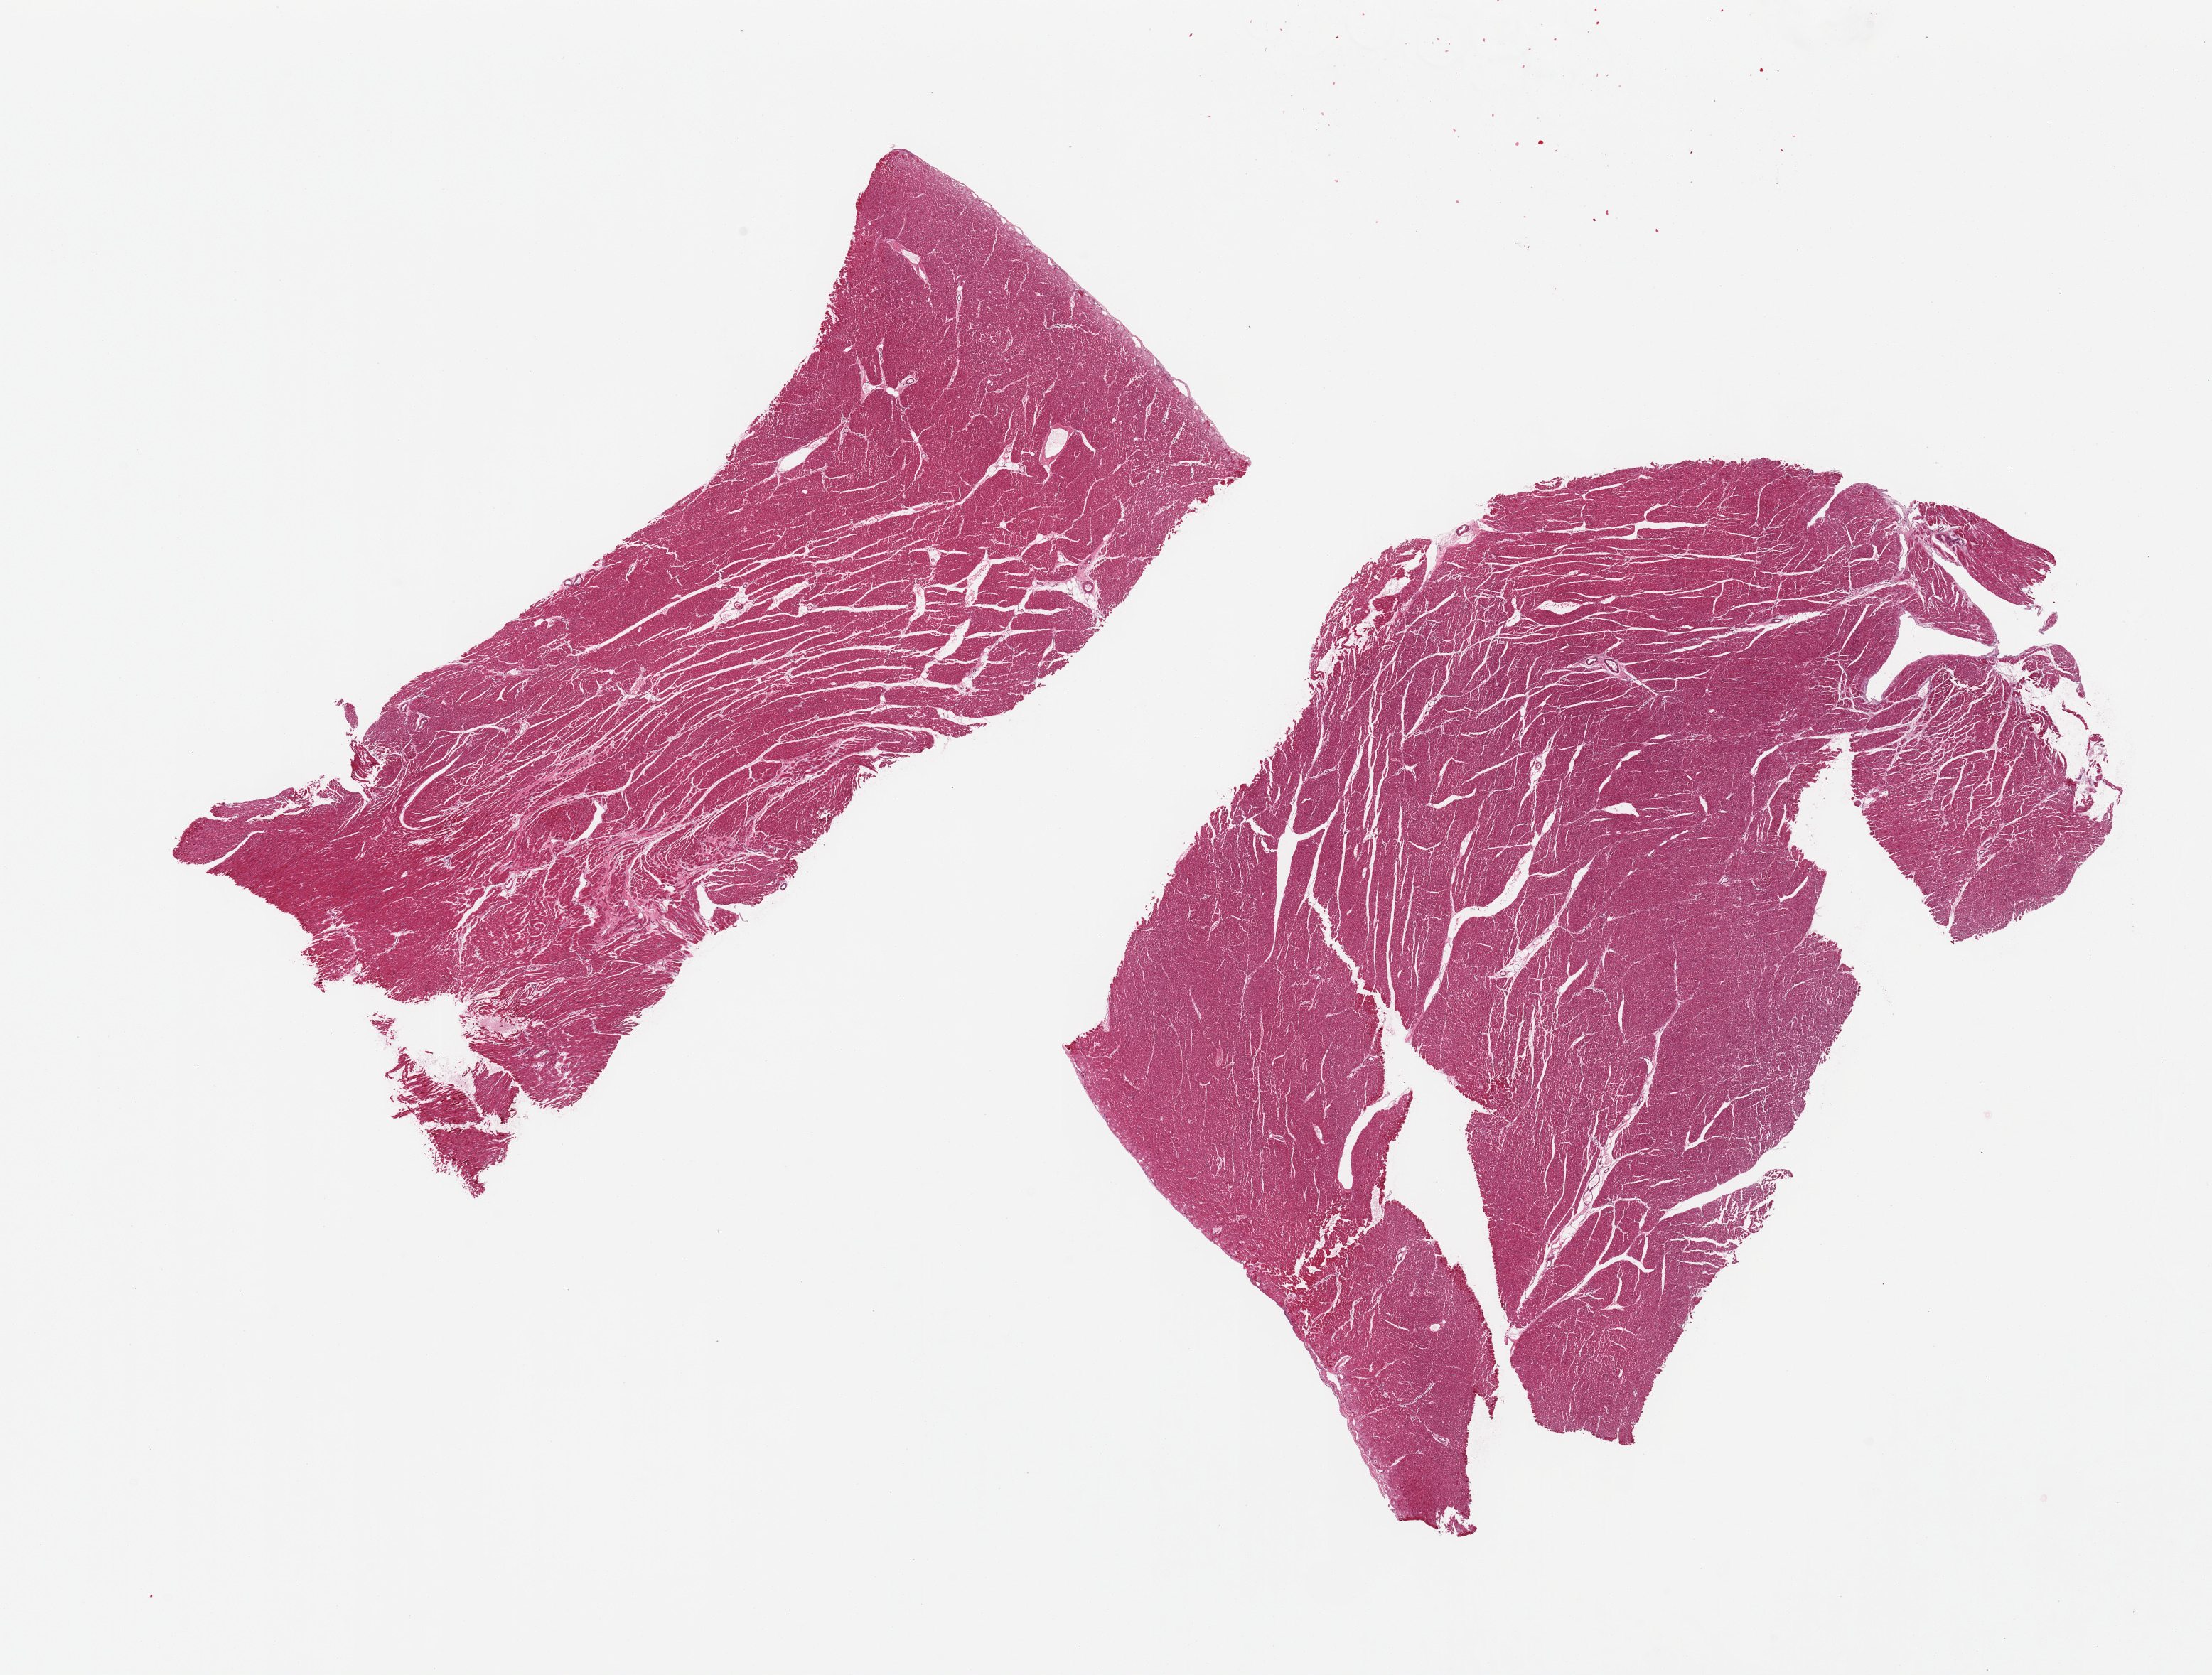
Digitized H&E-stained section, brightfield, low-resolution overview of the scanned area, about 24.6 x 18.6 mm, PAXgene-fixed paraffin-embedded (PFPE) section, sampled site (target tissue): heart, tissue donor sample. Donor sex: male.
Pathologist's review note for this sample: 2 pieces, contraction bands noted.